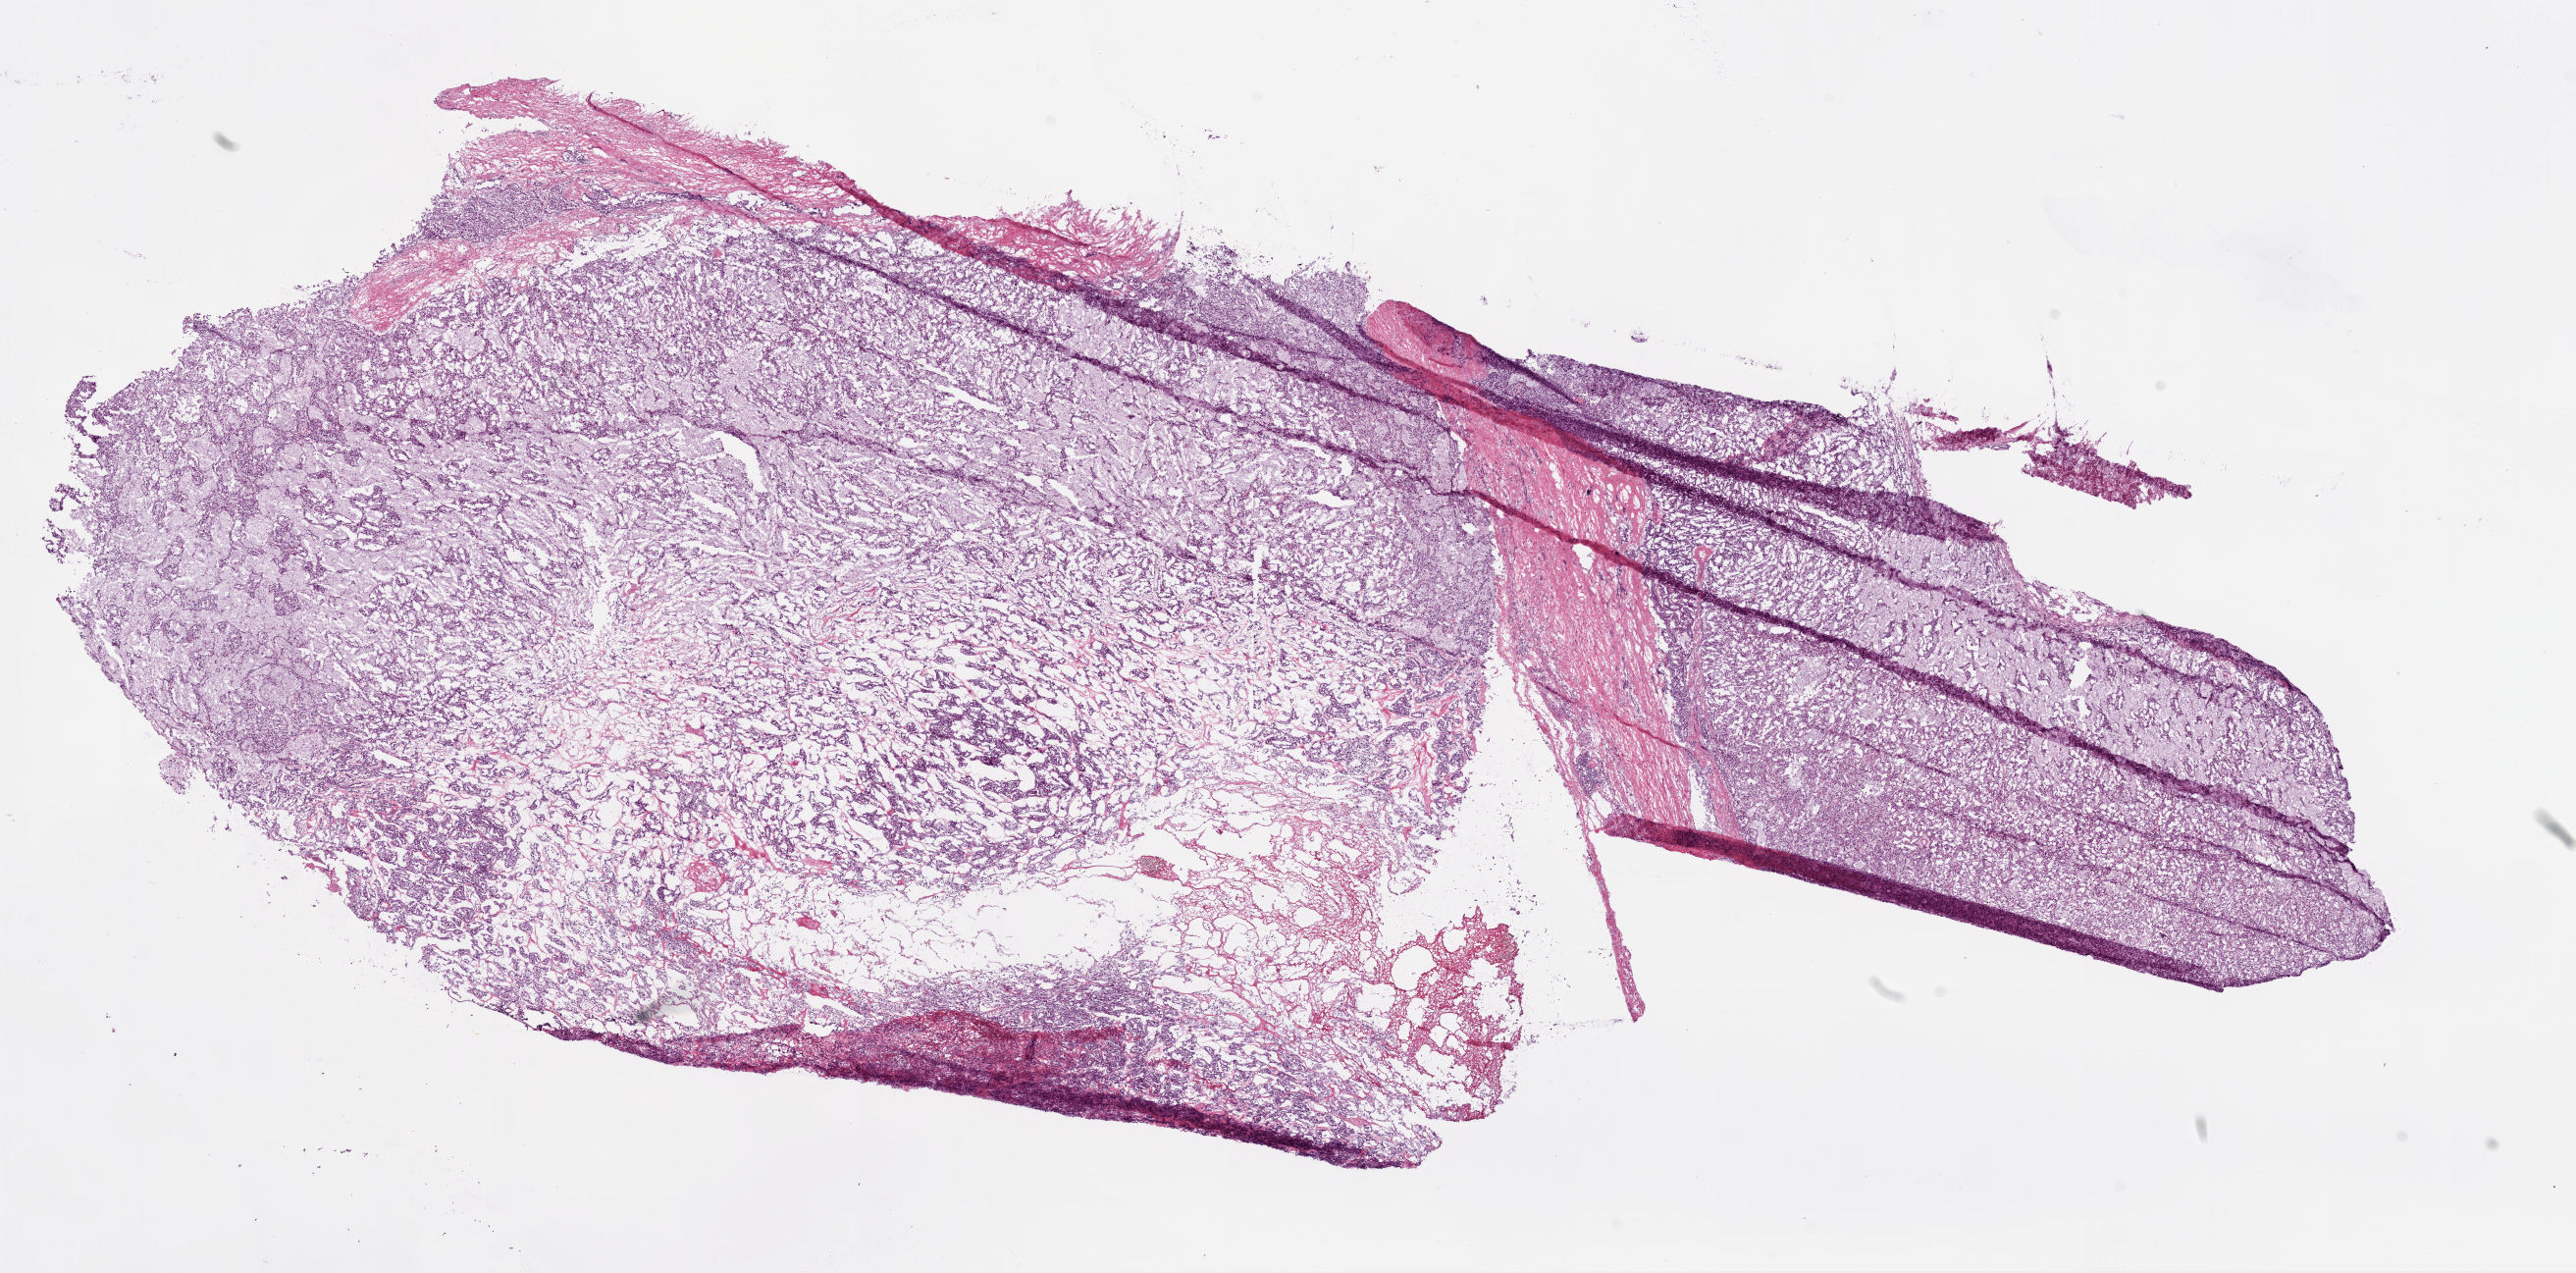
Whole-slide histology image, H&E, shown as a low-resolution overview of the whole scanned area (about 21.1 x 10.4 mm). Frozen section. Sample: primary tumour, kidney. Patient: female, age at initial diagnosis 39 years. Histologic grade: G3 (poorly differentiated). Slide review estimates, as recorded: tumour cells 88%, tumour nuclei 75%, normal cells 0%, stromal cells 12%, necrosis 0%. Infiltration values recorded for this section: lymphocyte infiltration 5%, monocyte infiltration 20%, neutrophil infiltration 0%.
* laterality: right
* histologic diagnosis: Clear cell adenocarcinoma, NOS
* AJCC pathologic stage: I (6th edition)